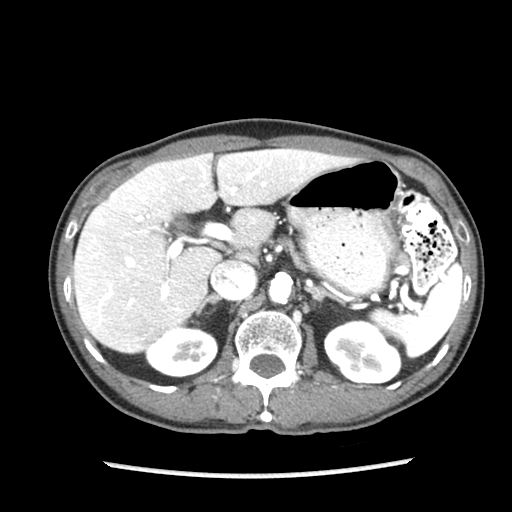
Contrast-enhanced abdominal CT (liver protocol), one axial slice; position 53 of 87 along the scan axis; 140 kVp; soft-tissue window (W 400 / L 40 HU); 2.5 mm slice thickness; 512 × 512 image matrix. Case-level facts recorded for this patient, not image findings: diagnosis: hepatocellular carcinoma (patient treated with transarterial chemoembolisation; whether this scan precedes or follows treatment is not stated here); TNM stage (as recorded): Stage-IIIB.
Outlined on this slice (semi-automatically segmented with operator editing):
- liver parenchyma outside the tumour (the mass and vessels are separate outlines, so this box may not span the whole liver): bounding box [x1, y1, x2, y2] px = [72, 148, 355, 352]
- liver vessels: [93, 162, 303, 320]